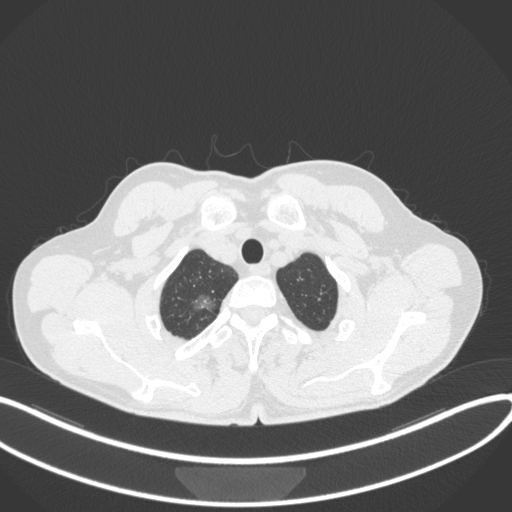
Chest CT, one axial slice. Position 349 of 407 along the scan axis. Reconstruction kernel B31f. 120 kVp. Lung window (W 1500 / L -600 HU). 1 mm slice thickness. 512 × 512 image matrix, field of view 400 × 400 mm. Patient: male, 58 years. From the clinical record (not read from this slice): clinical TNM (as recorded): T1c N0 M0; histopathological grade: G1-2.
Annotated regions visible in this slice (bounding box drawn by a radiologist):
- lung tumour (recorded histology: adenocarcinoma): bounding box [x1, y1, x2, y2] px = [185, 283, 219, 321]